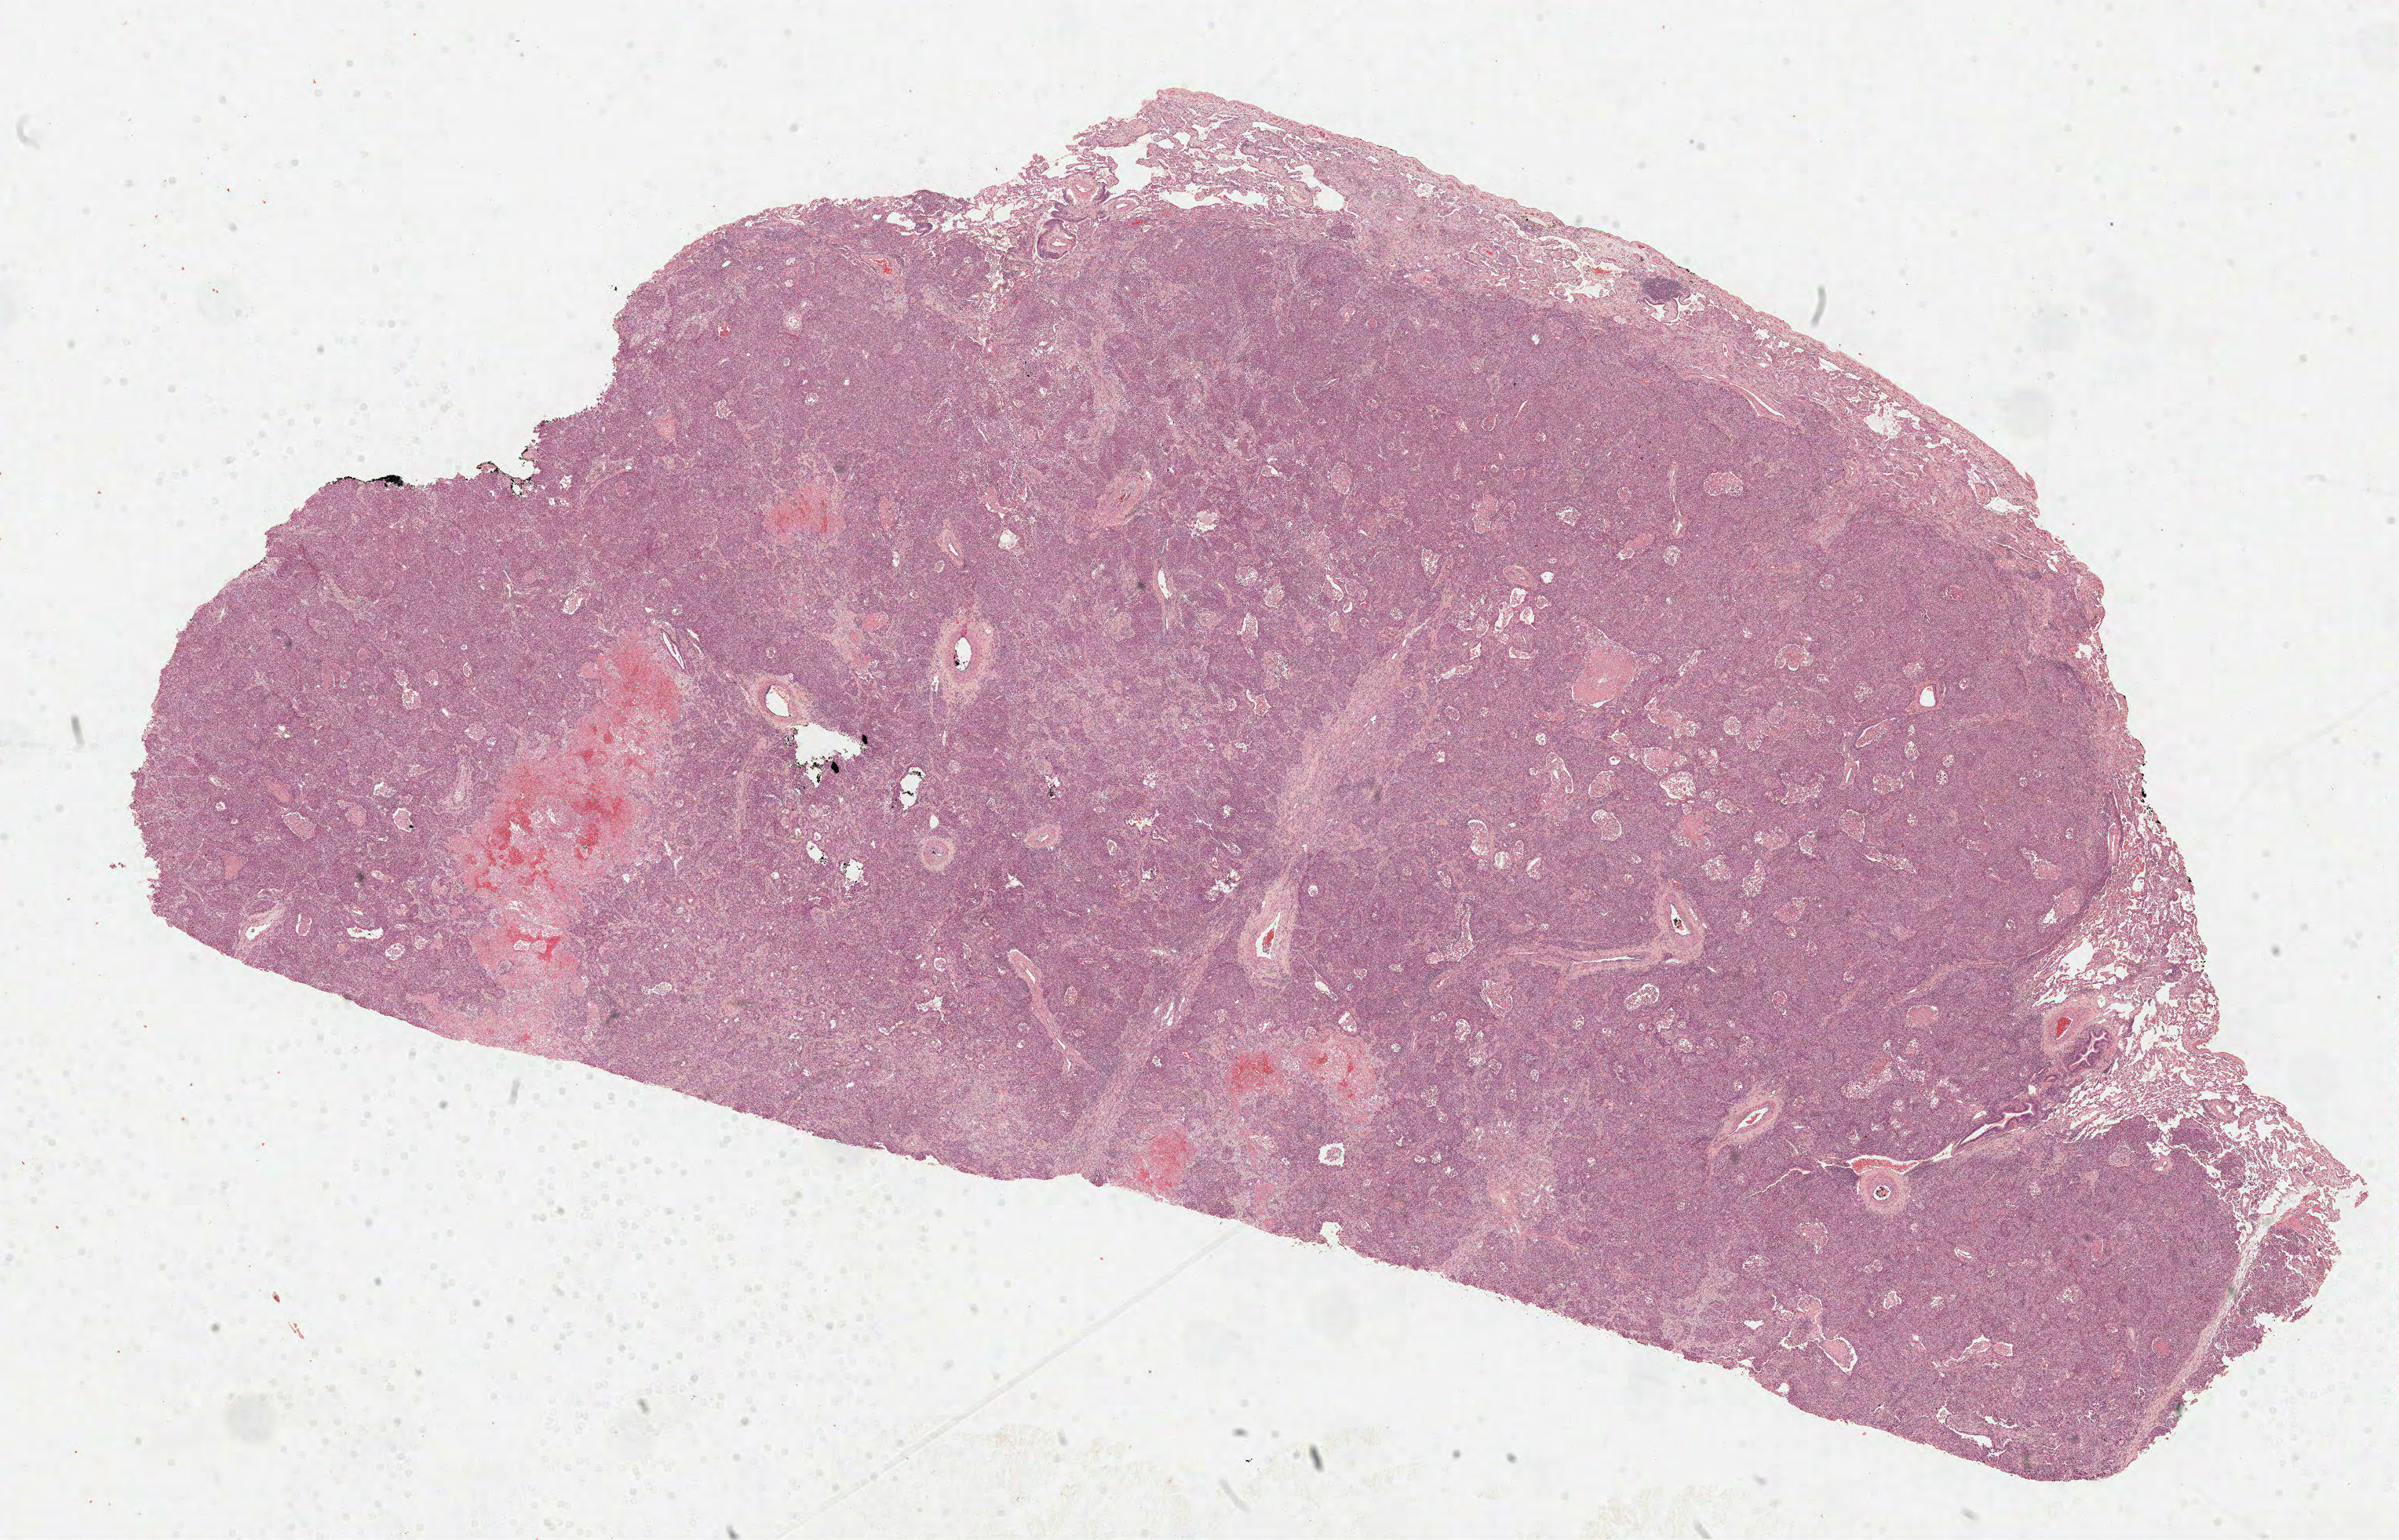
Digitized H&E-stained tissue section (whole slide), shown as a low-resolution overview of the whole scanned area (about 24.7 x 15.8 mm); formalin-fixed paraffin-embedded (FFPE) diagnostic section; lung, primary tumour sample. Male patient; age at initial diagnosis 68 years.
Pathologic diagnosis: Adenocarcinoma, NOS (lower lobe, lung).